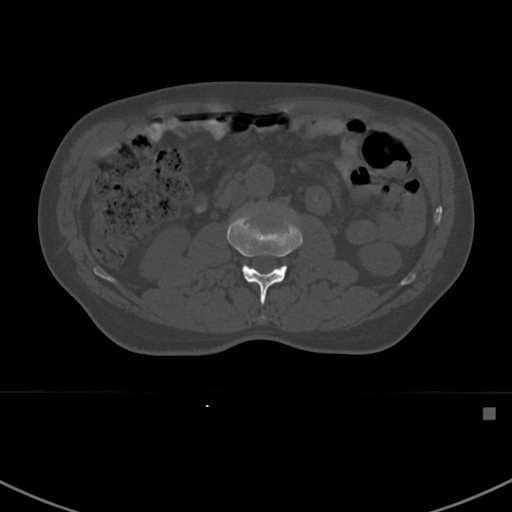
CT including the spine, one axial slice; slice 283 of 412 in the series (ordered by position); reconstruction kernel Br40s; bone window (W 1800 / L 400 HU); 1.5 mm slice thickness; 512 × 512 image matrix, field of view 358 × 358 mm. Male patient, age 59 years. Case-level facts recorded for this patient, not image findings: primary cancer: prostate.
Structures marked on this image (semi-automatic segmentation, software-assisted and operator-edited):
- L2 vertebra: bounding box <227,211,303,321> (left, top, right, bottom; pixels)